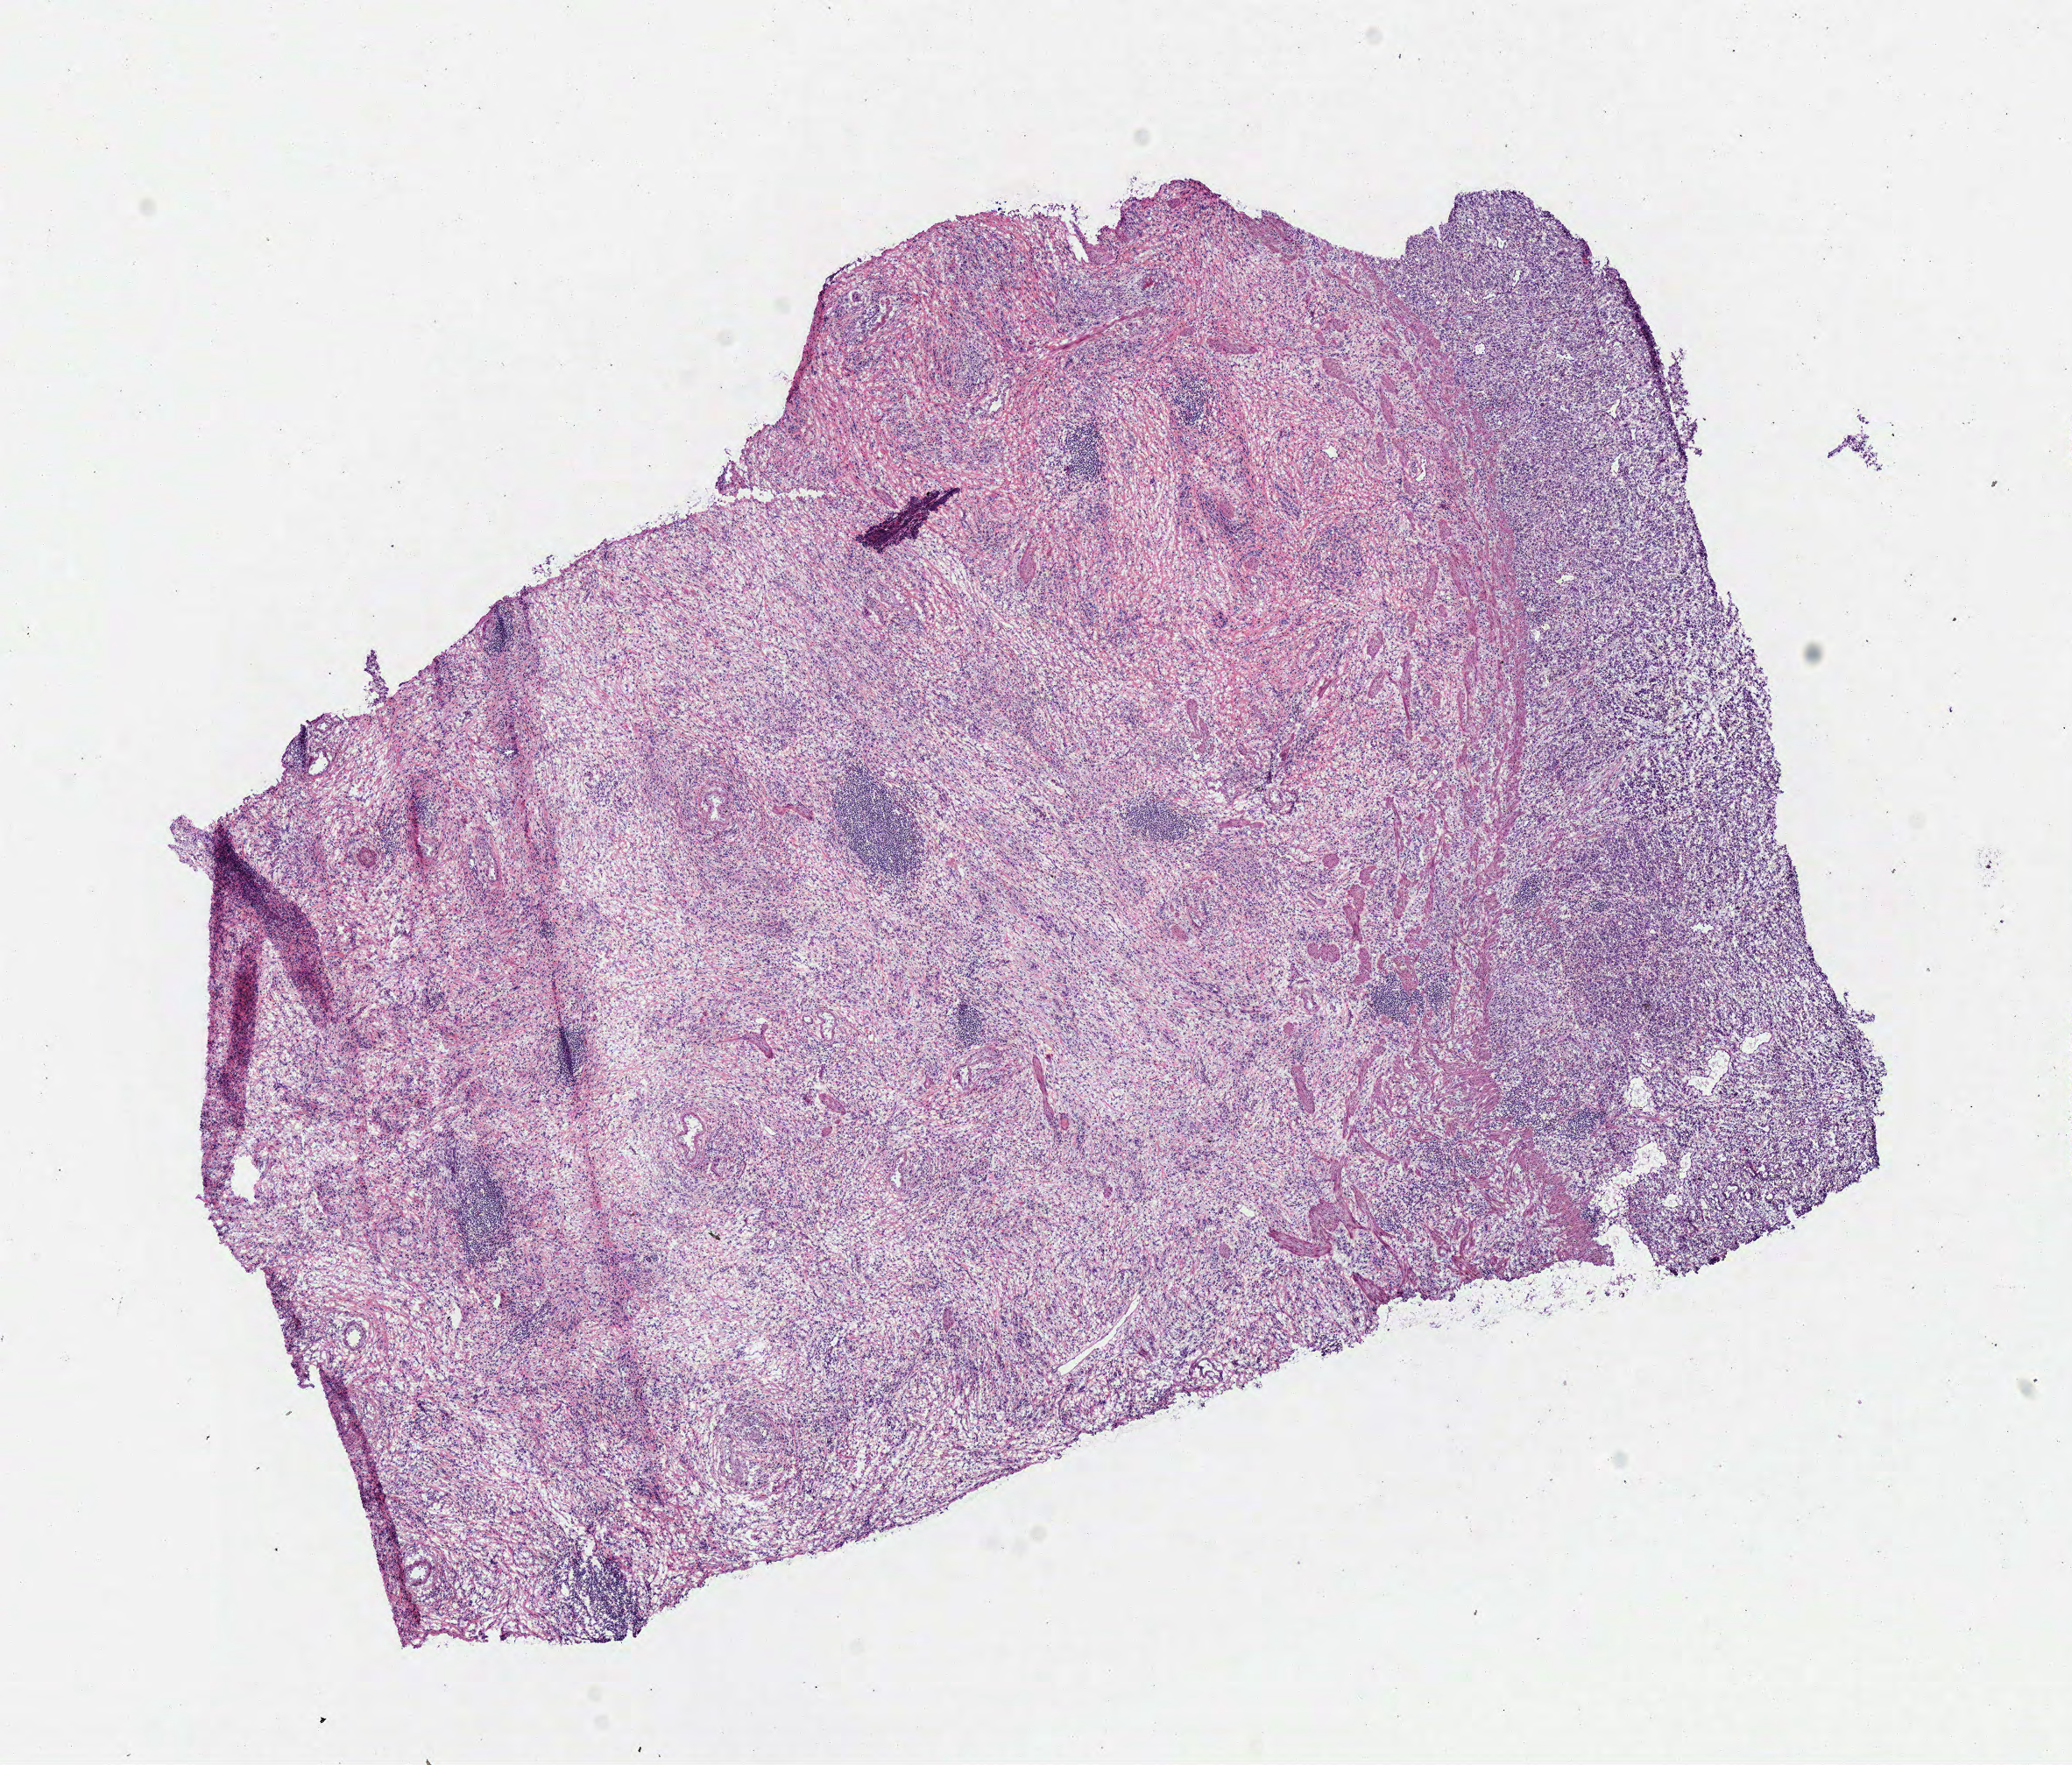
Whole-slide histology image, H&E — whole scanned area (about 9.3 x 7.9 mm, from a 40x scan) shown as a low-resolution overview; frozen section; stomach, primary tumour sample. Patient: male, age at initial diagnosis 53 years. Histologic grade: G3 (poorly differentiated). Pathologist review of this section (percent, as recorded): tumour cells 75%, tumour nuclei 75%, normal cells 0%, stromal cells 25%, necrosis 0%.
Histologic diagnosis: Carcinoma, diffuse type (gastric antrum). Lymph nodes positive (case pathology): 6 of 16 examined. AJCC pathologic stage: II (6th edition).